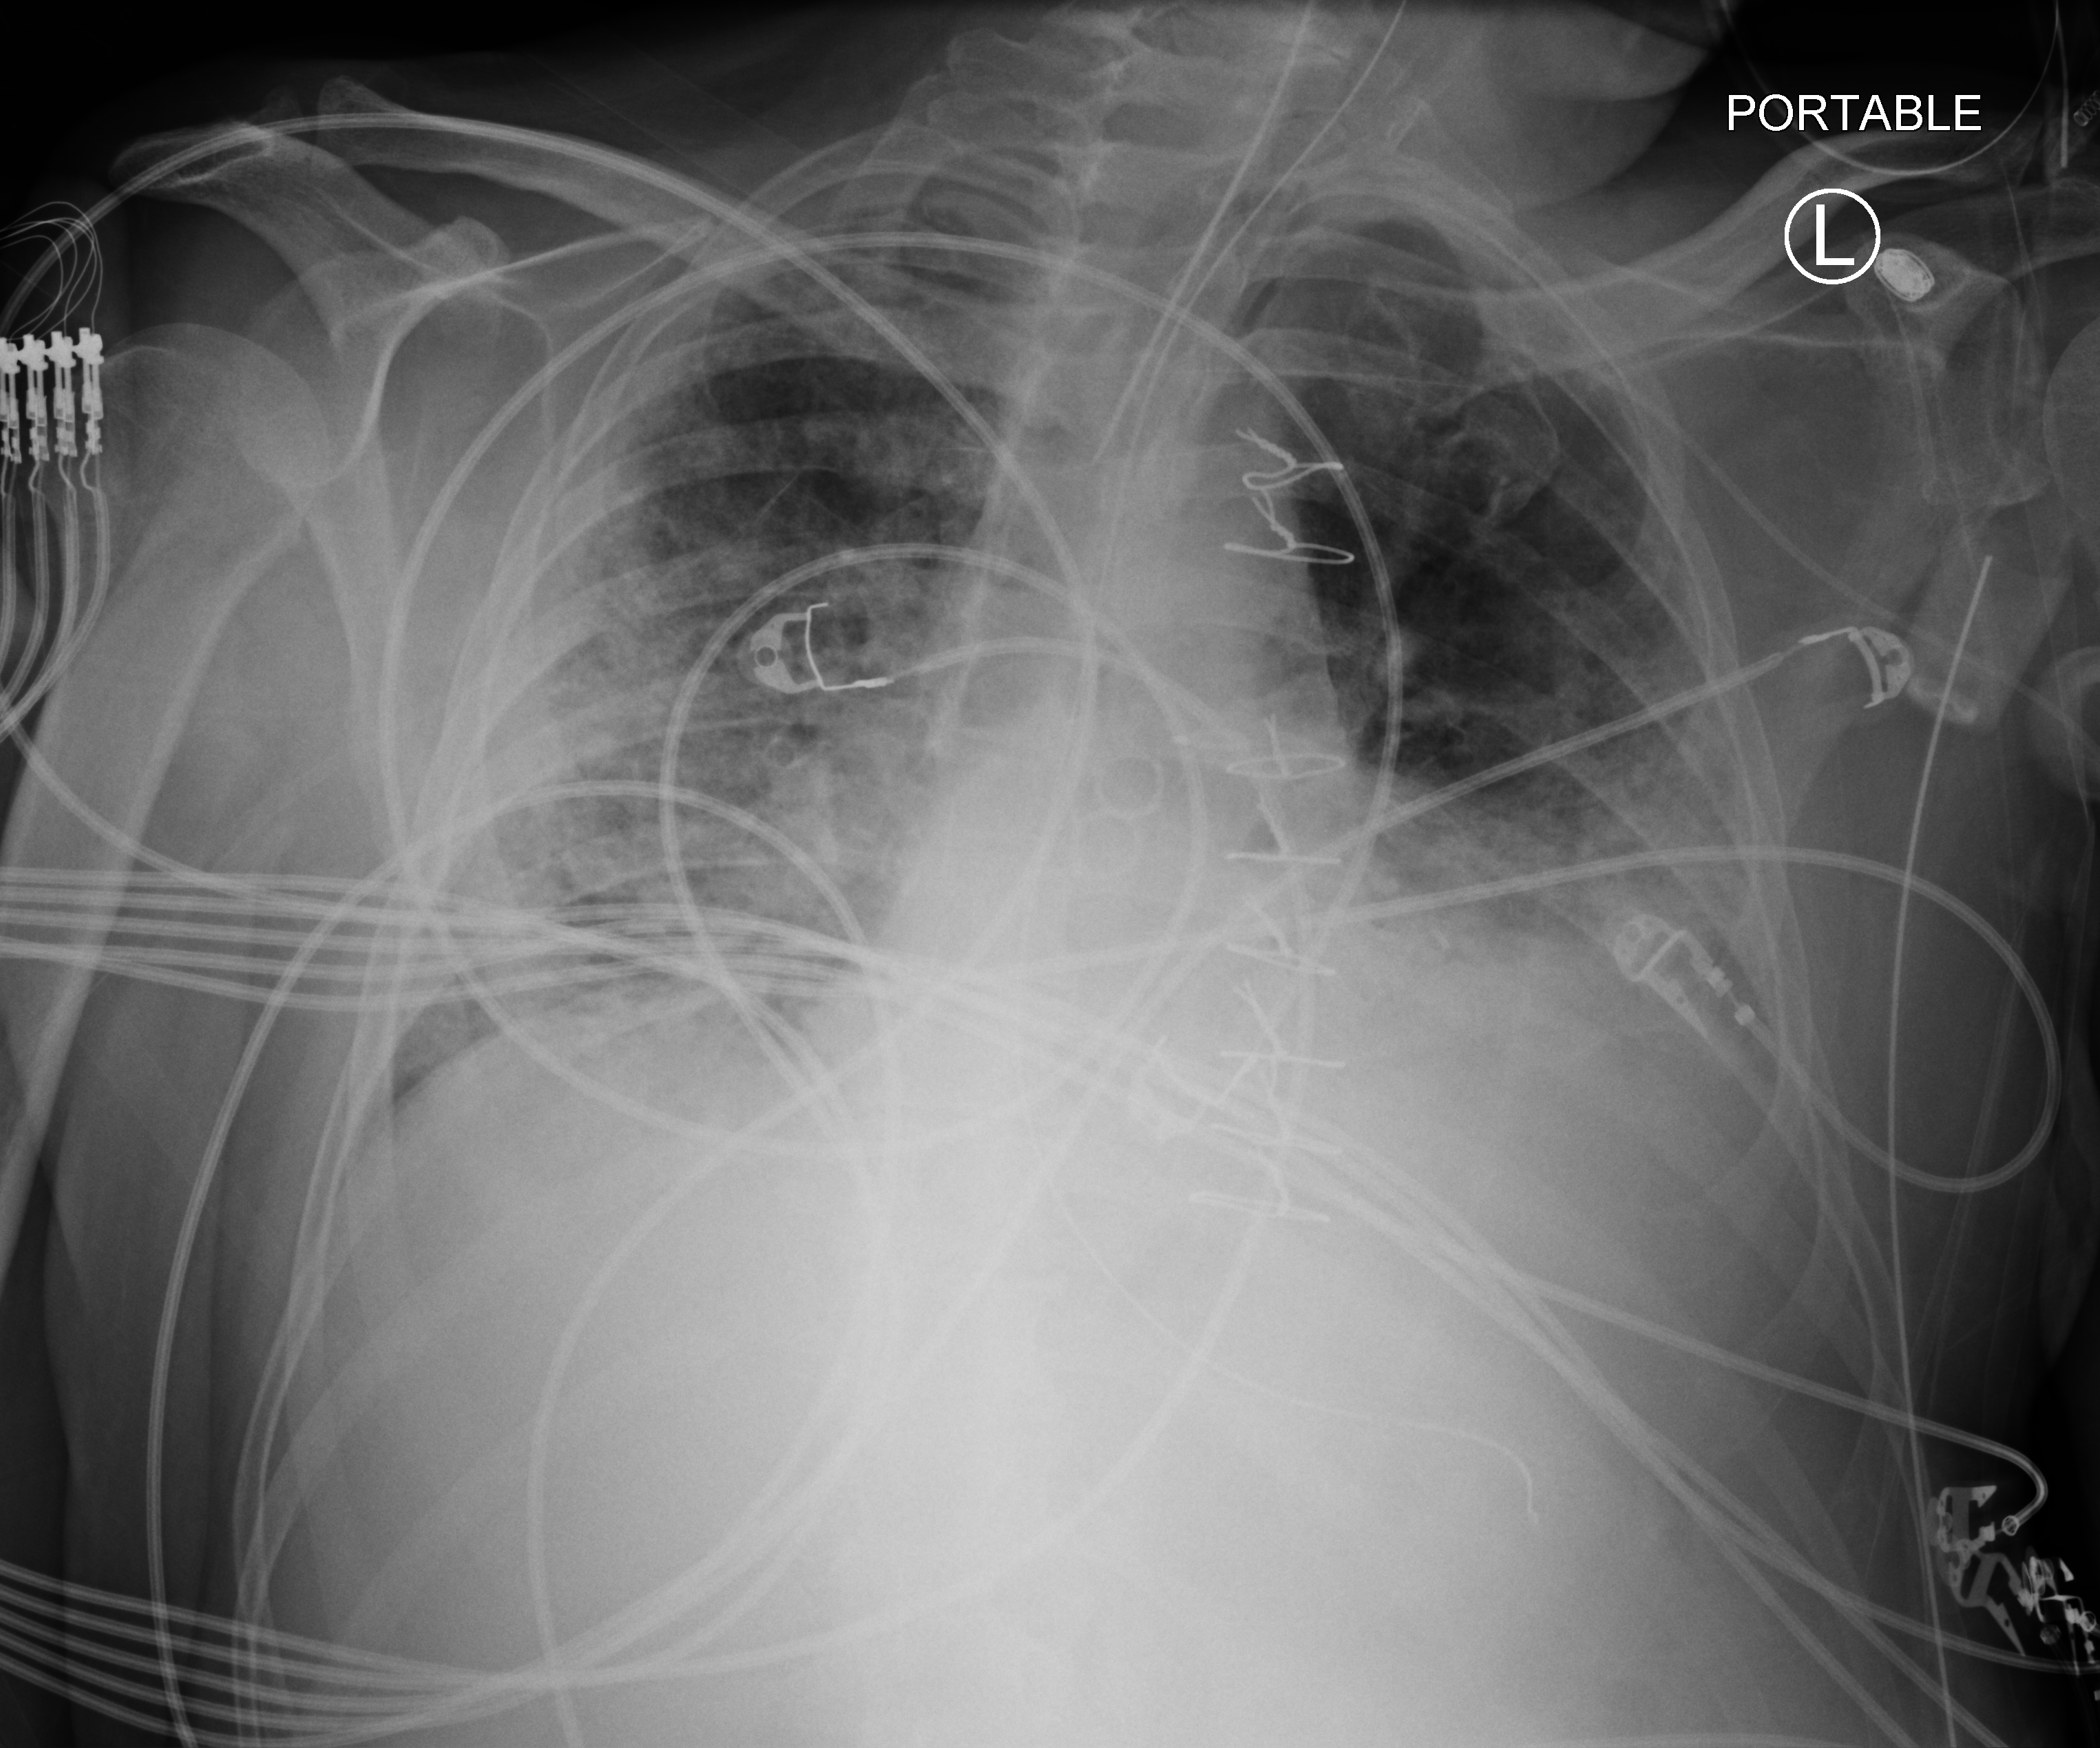
Chest X-ray (portable), anteroposterior (AP) projection. Male patient hospitalised with COVID-19, age 18–59 years.
Hospital-stay facts (about this admission, not read from this image; timing relative to this image not recorded): COPD (admission record): yes.